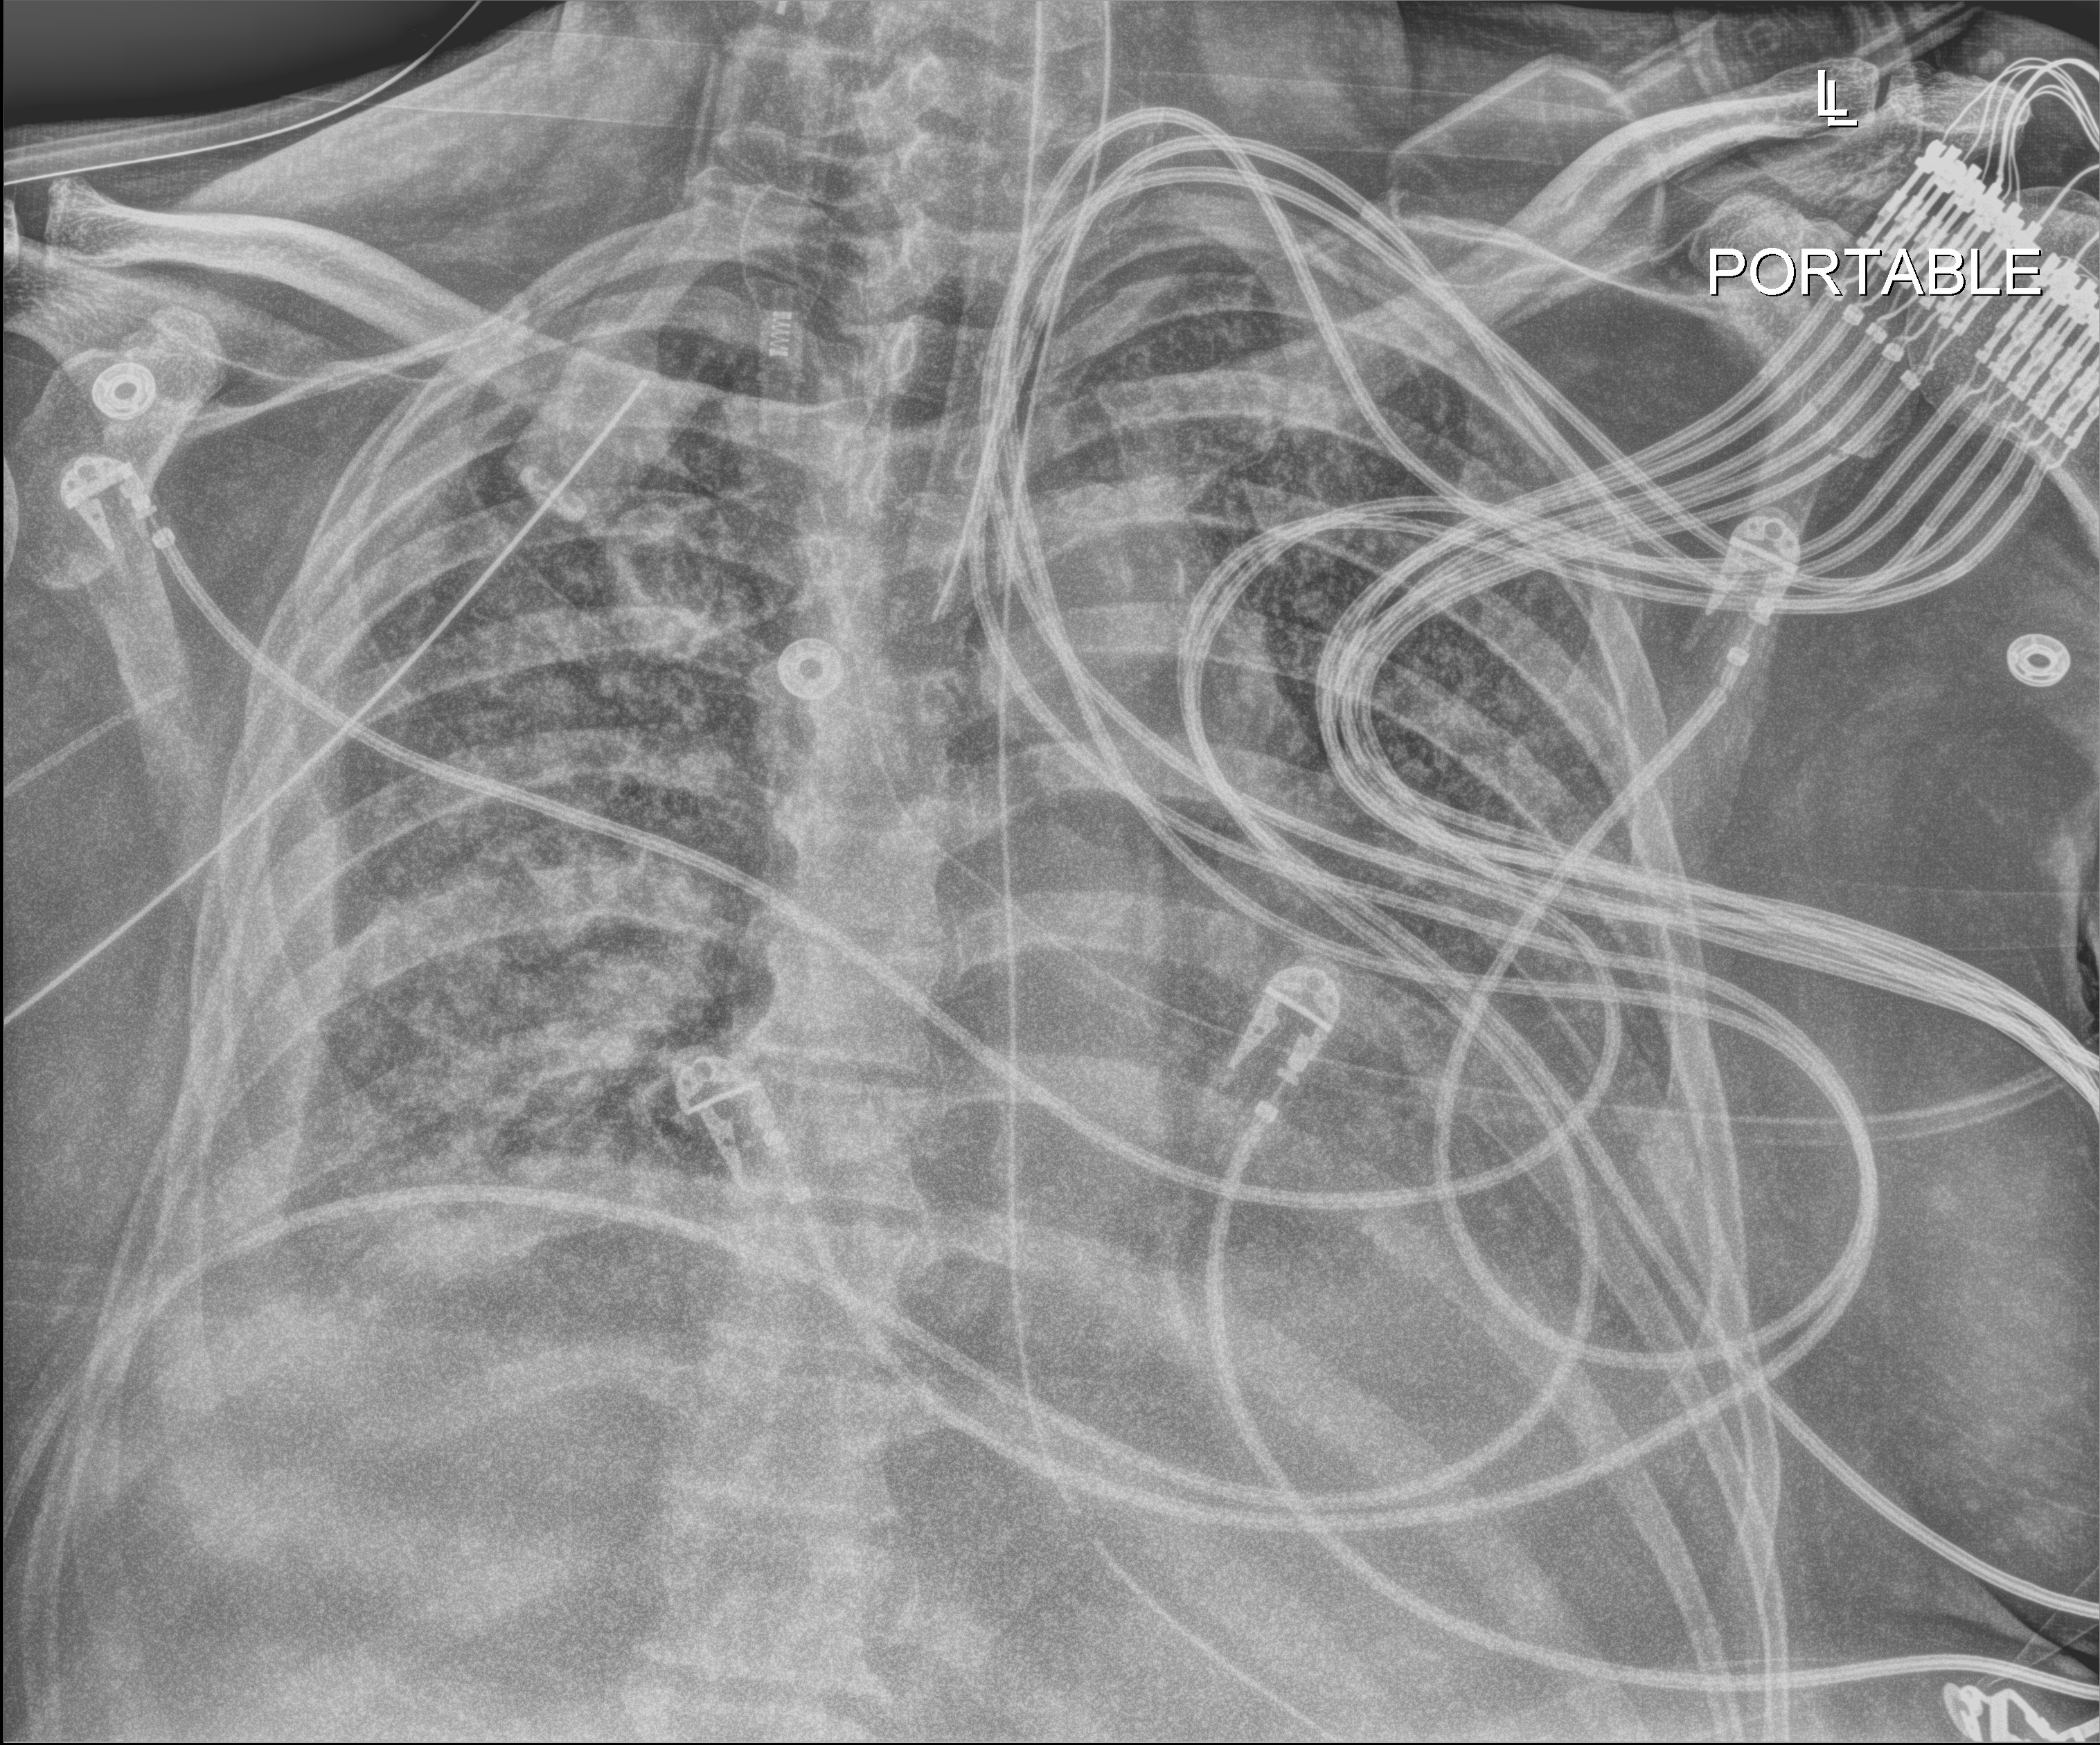
Chest X-ray (portable), anteroposterior (AP) projection. Patient hospitalised with COVID-19; male, aged 60–74 years.
Hospital-stay facts (about this admission, not read from this image; timing relative to this image not recorded):
- other chronic lung disease (admission record): no